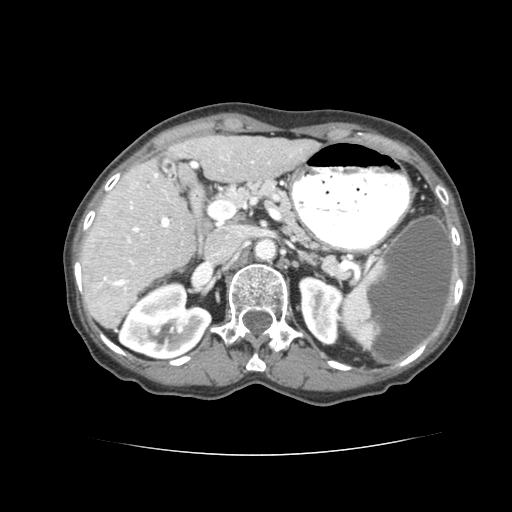
Contrast-enhanced abdominal CT (liver protocol), one axial slice; position 40 of 77 along the scan axis; reconstruction kernel STANDARD; soft-tissue window (W 400 / L 40 HU); 2.5 mm slice thickness; 512 × 512 image matrix, field of view 340 × 340 mm. Case-level facts recorded for this patient, not image findings: diagnosis: hepatocellular carcinoma (patient treated with transarterial chemoembolisation; whether this scan precedes or follows treatment is not stated here); TNM stage (as recorded): Stage-I; Child-Pugh class: A; tumour differentiation: well differentiated; tumour nodularity: uninodular.
Annotated regions visible in this slice (semi-automatic segmentation, software-assisted and operator-edited):
- liver parenchyma outside the tumour (the mass and vessels are separate outlines, so this box may not span the whole liver): bounding box (x1, y1, x2, y2) in pixels: (78, 136, 316, 325)
- liver vessels: (100, 161, 270, 278)